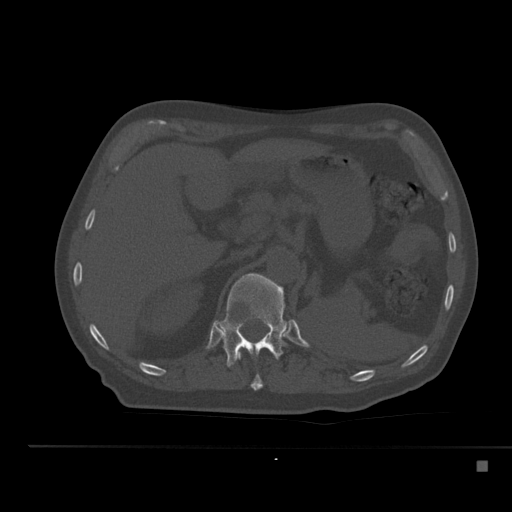
CT including the spine, one axial slice. Reconstruction kernel Br40s. 120 kVp. Bone window (W 1800 / L 400 HU). 512 × 512 image matrix, field of view 408 × 408 mm. Male patient, age 70 years. From the clinical record (not read from this slice): primary cancer: renal; vertebrae with lytic lesions (as recorded): T4, T6, T10, T12, L3, L4, L5.
Structures marked on this image (semi-automatically segmented with operator editing):
- T11 vertebra: bounding box (x1, y1, x2, y2) in pixels: (239, 354, 263, 390)
- T12 vertebra: (215, 273, 289, 367)